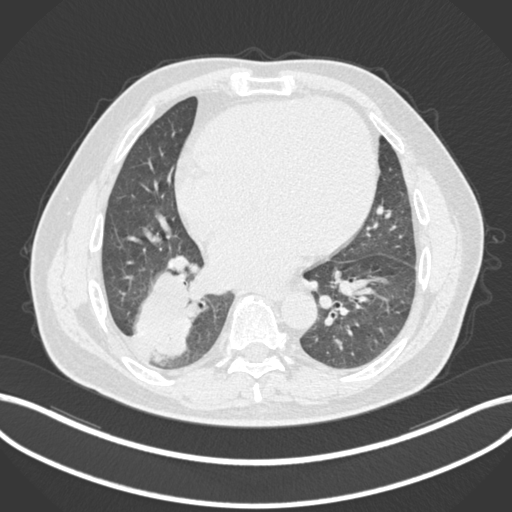
Chest CT, one axial slice; position 64 of 200 along the scan axis; reconstruction kernel B30f; 120 kVp; lung window (W 1500 / L -600 HU); 1 mm slice thickness; 512 × 512 image matrix. Male patient, age 59 years.
Annotated regions visible in this slice (bounding box drawn by a radiologist):
- lung tumour (recorded histology: adenocarcinoma): bounding box [x1, y1, x2, y2] px = [135, 266, 200, 359]